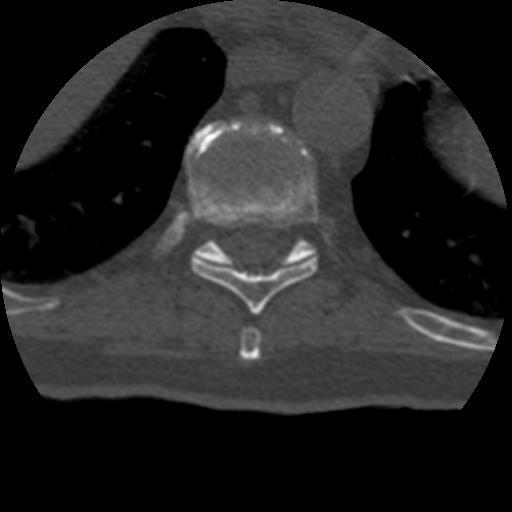
CT including the spine, one axial slice; position 233 of 399 along the scan axis; reconstruction kernel STANDARD; bone window (W 1800 / L 400 HU); 1.25 mm slice thickness; 512 × 512 image matrix. Patient age 69 years. From the clinical record (not read from this slice): primary cancer: prostate.
Outlined on this slice (semi-automatic segmentation, software-assisted and operator-edited):
- T10 vertebra: box from (x=188, y=121) to (x=317, y=267) px
- T8 vertebra: (x=240, y=327)–(x=262, y=361)
- T9 vertebra: (x=191, y=148)–(x=318, y=315)